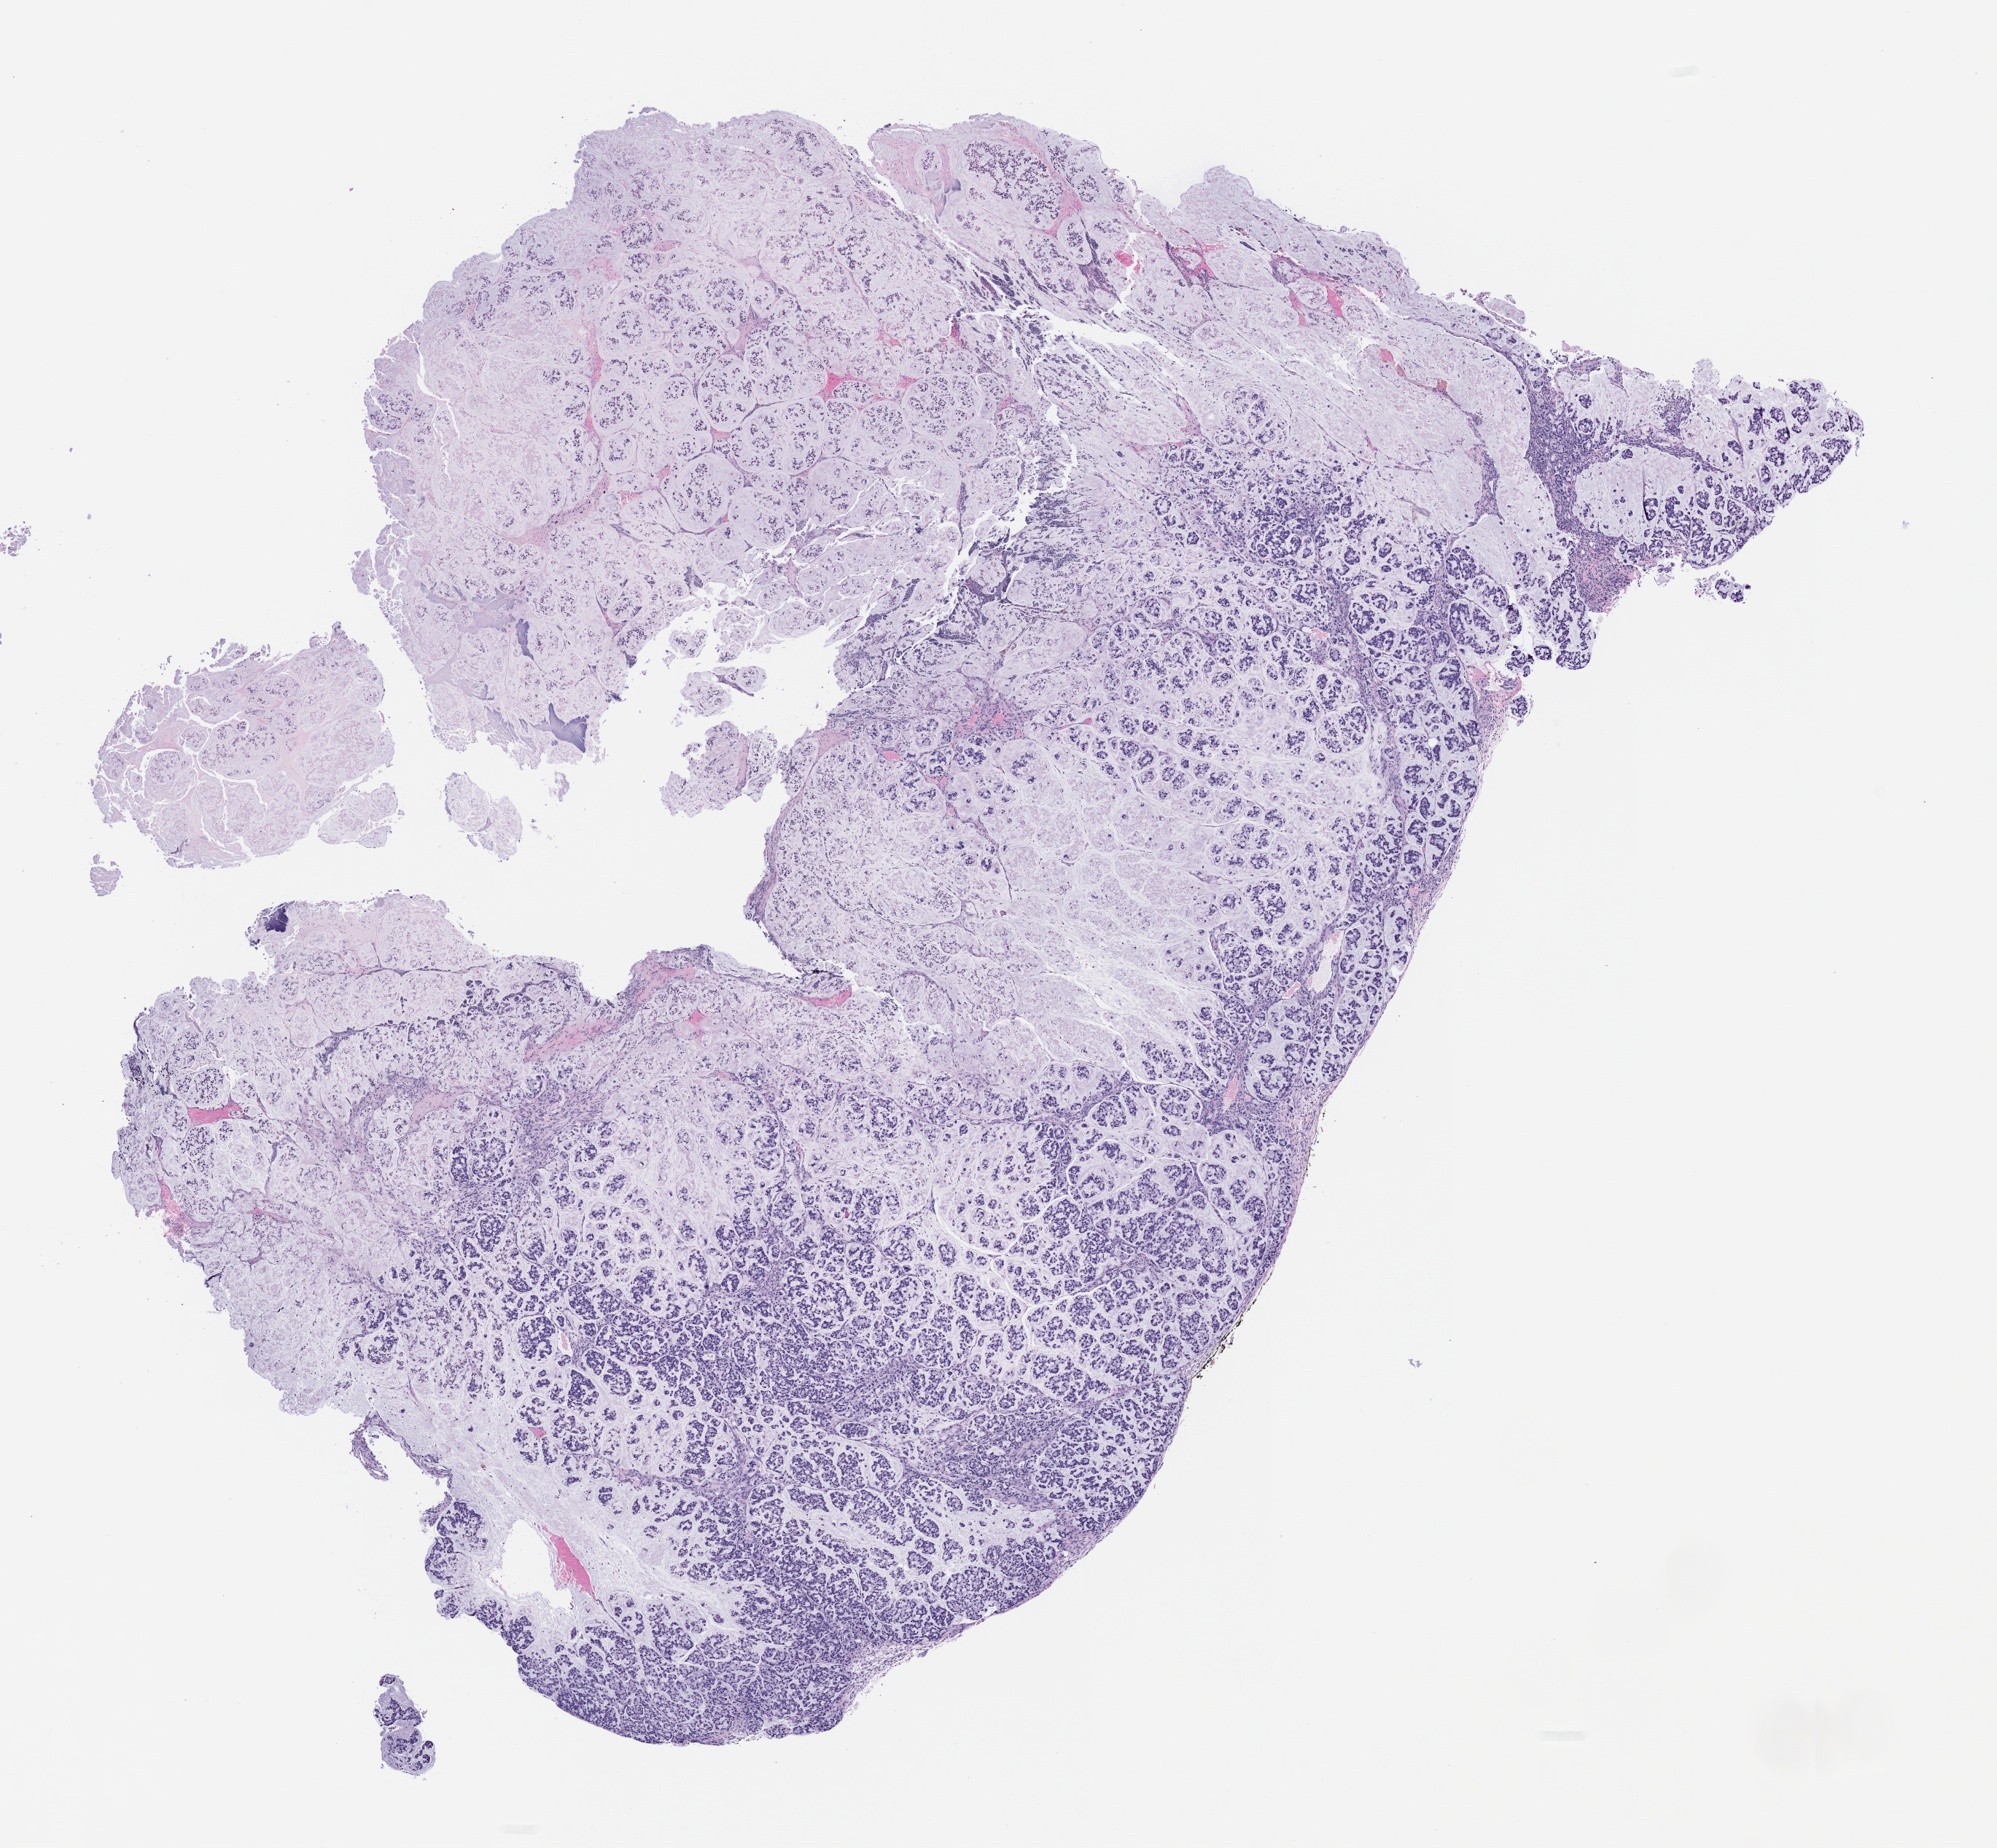
H&E whole-slide image of a patient-derived xenograft (PDX) tumor grown in a mouse, passage 1, low-resolution overview of the scanned area, about 11.0 x 10.2 mm, formalin-fixed, paraffin-embedded (FFPE) tissue, tumor site category: colon.
• originating patient diagnosis: Colon Adenocarcinoma